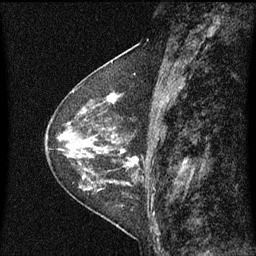
Breast MRI (dynamic contrast-enhanced), one sagittal slice. Slice 28 of 60 in the series (ordered by position). Dynamic contrast-enhanced series, image 2 of 3 at this slice position (ordered by acquisition). 1.5 T. TE 4.2 ms, TR 8 ms. 2 mm slice thickness. 256 × 256 image matrix. Female patient, age 48 years.
Structures marked on this image (semi-automatically segmented with operator editing):
- analysis volume of interest (the breast-tissue region the enhancement analysis was run in; not a lesion): box from (x=103, y=74) to (x=144, y=139) px
- tumour enhancement mask (voxels above the 70 % enhancement threshold inside the analysis volume of interest): (x=106, y=94)–(x=122, y=103)